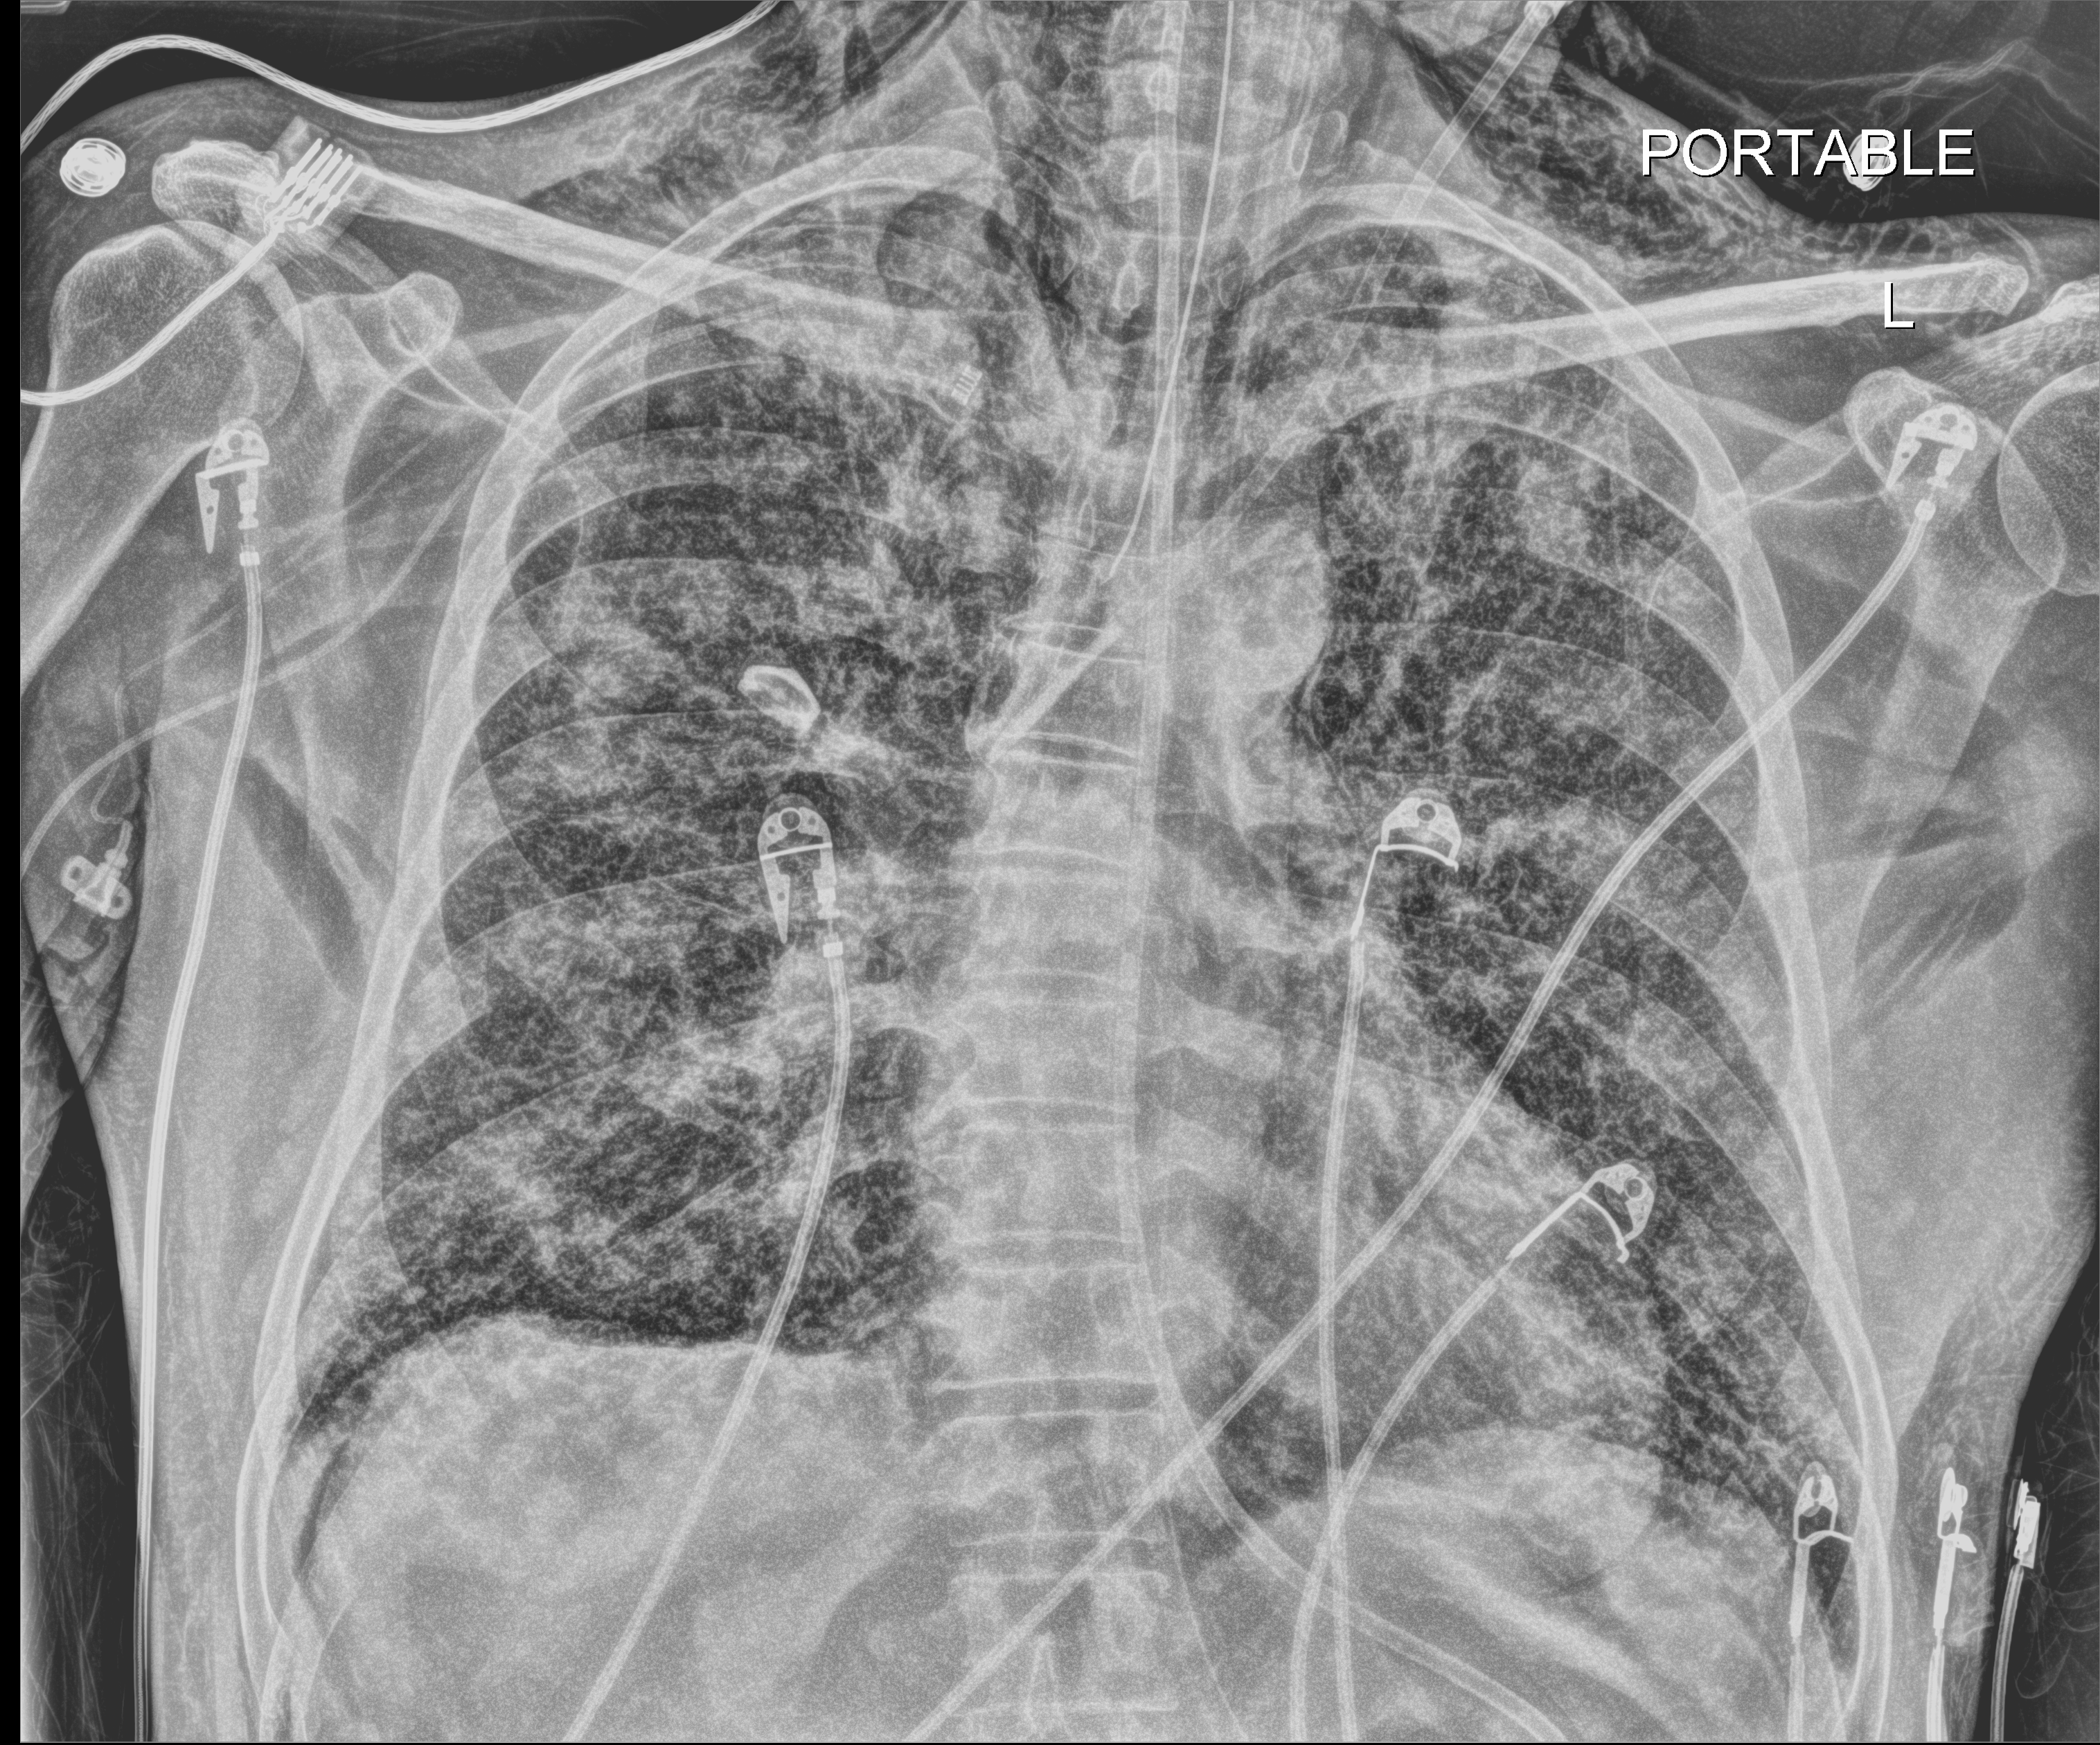
Bedside chest radiograph (digital radiography). Patient hospitalised with COVID-19; male, aged 18–59 years.
Admission-level facts for this patient (not findings on this image; timing relative to this image not recorded): mechanically ventilated during this hospital stay: yes; chronic kidney disease (admission record): no; admitted to intensive care during this hospital stay: yes.